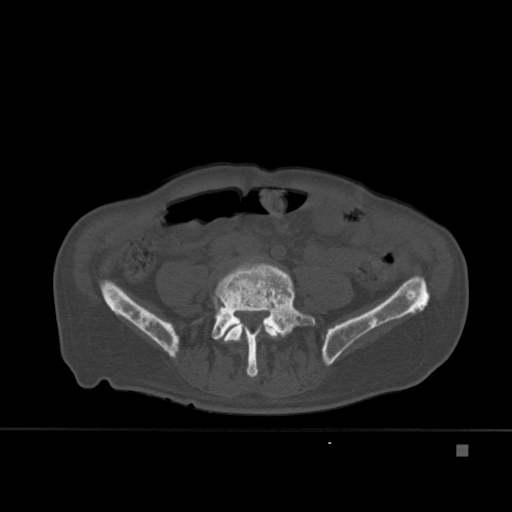
CT including the spine, one axial slice. Bone window (W 1800 / L 400 HU). 1.5 mm slice thickness. 512 × 512 image matrix. Patient: male, 75 years. Case-level facts recorded for this patient, not image findings: primary cancer: prostate.
Outlined on this slice (semi-automatic segmentation, software-assisted and operator-edited):
- L4 vertebra: box from (x=224, y=323) to (x=279, y=378) px
- L5 vertebra: (x=194, y=262)–(x=315, y=377)
- T7 vertebra: (x=264, y=315)–(x=274, y=325)